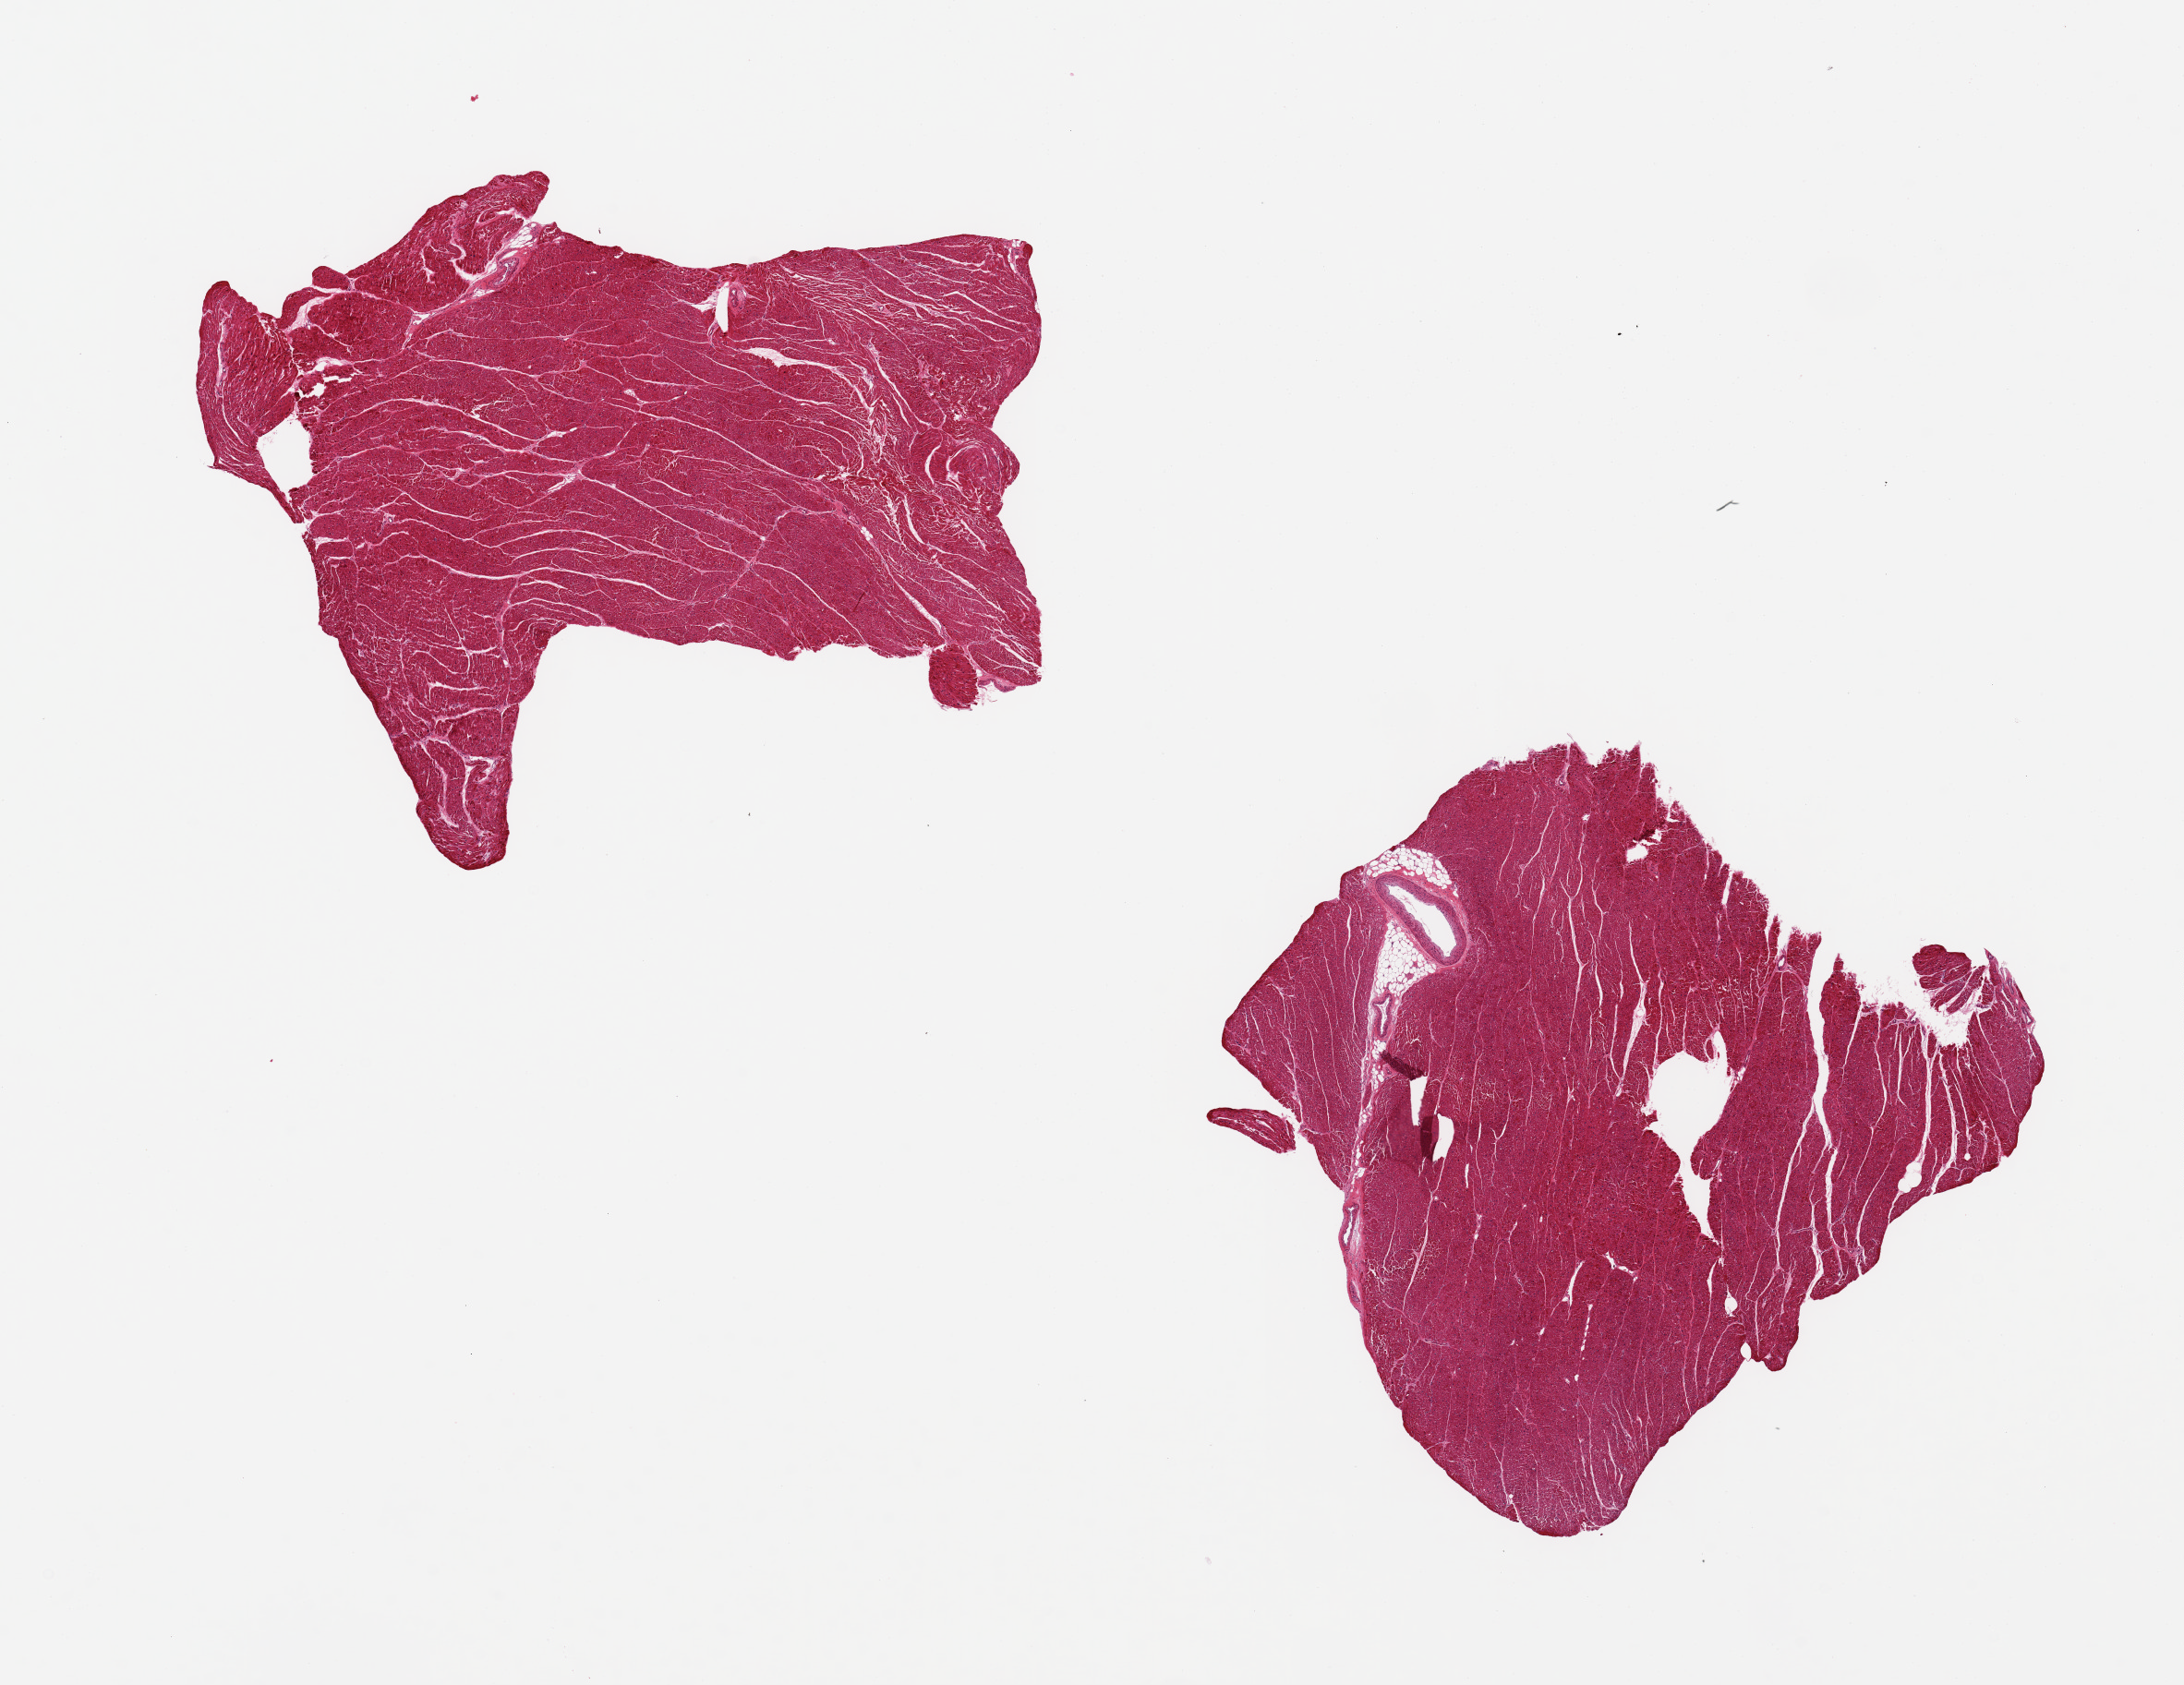
Hematoxylin and eosin (H&E) whole-slide image — a low-resolution overview of the entire scanned area, about 18.7 x 14.4 mm (slide scanned at 20x); PAXgene-fixed paraffin-embedded (PFPE) section; section of heart (target tissue); donor tissue sample.
Pathologist's review note for this sample: 2 pieces, 7x6 & 6x5.5mm; <5% internal adipose.